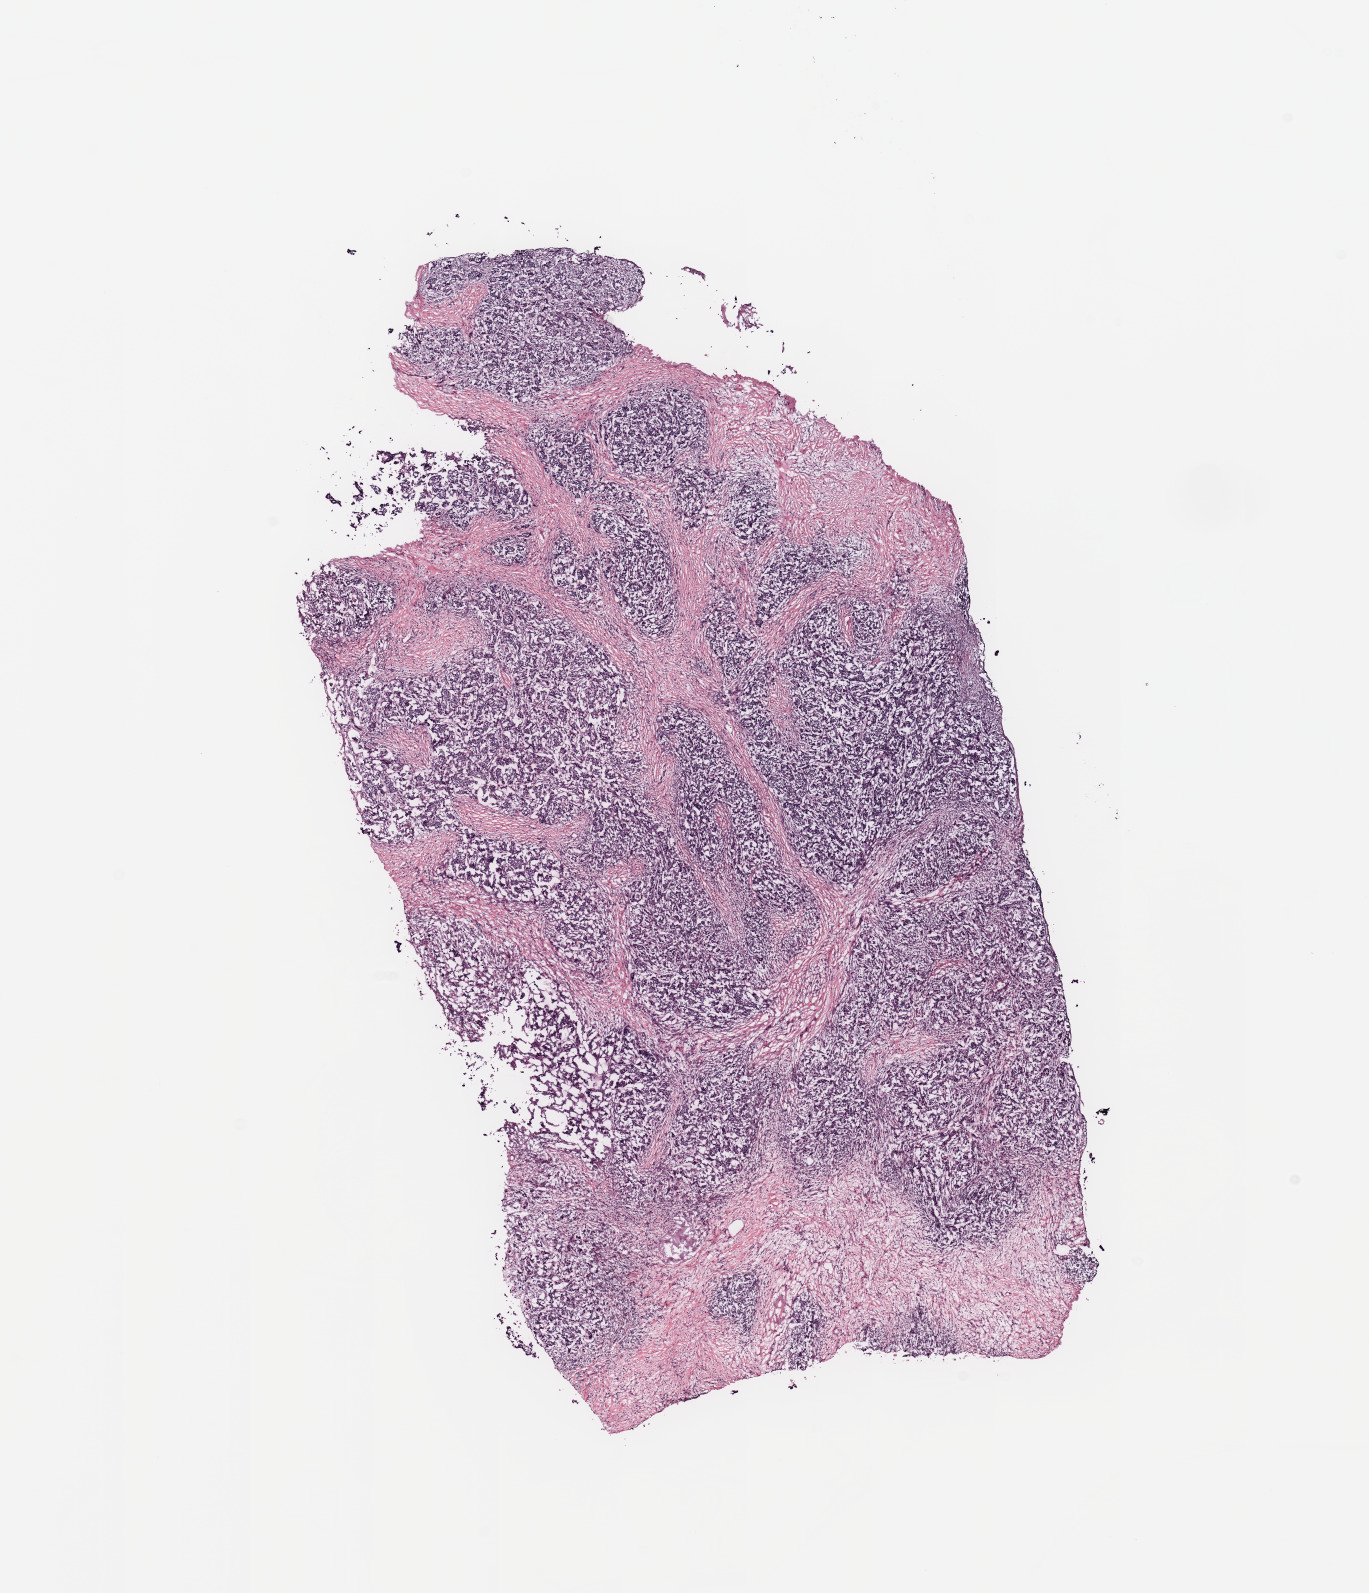
Whole-slide histology image, H&E-stained — whole scanned area (about 10.8 x 12.6 mm, slide scanned at 20x) shown as a low-resolution overview. Patient: female, age 86 years.
* specimen: tumour tissue sample, breast